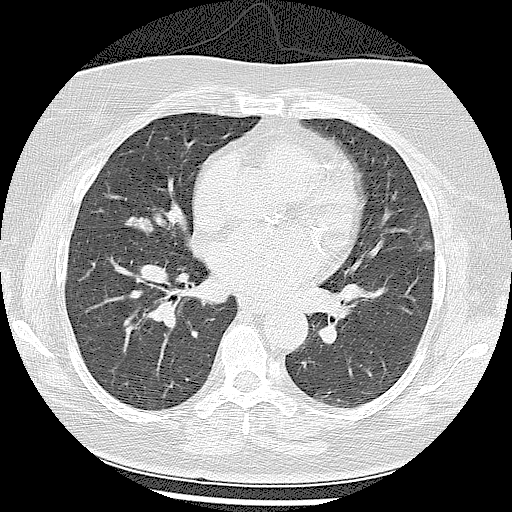
Low-dose screening chest CT, one axial slice; position 48 of 102 along the scan axis; reconstruction kernel LUNG; 120 kVp; lung window (W 1500 / L -600 HU); 2.5 mm slice thickness; 512 × 512 image matrix, field of view 350 × 350 mm.
Structures marked on this image (outlined manually by an expert reader):
- lesion 1 (tumor, middle lobe of right lung): bounding box <123,216,154,236> (left, top, right, bottom; pixels)